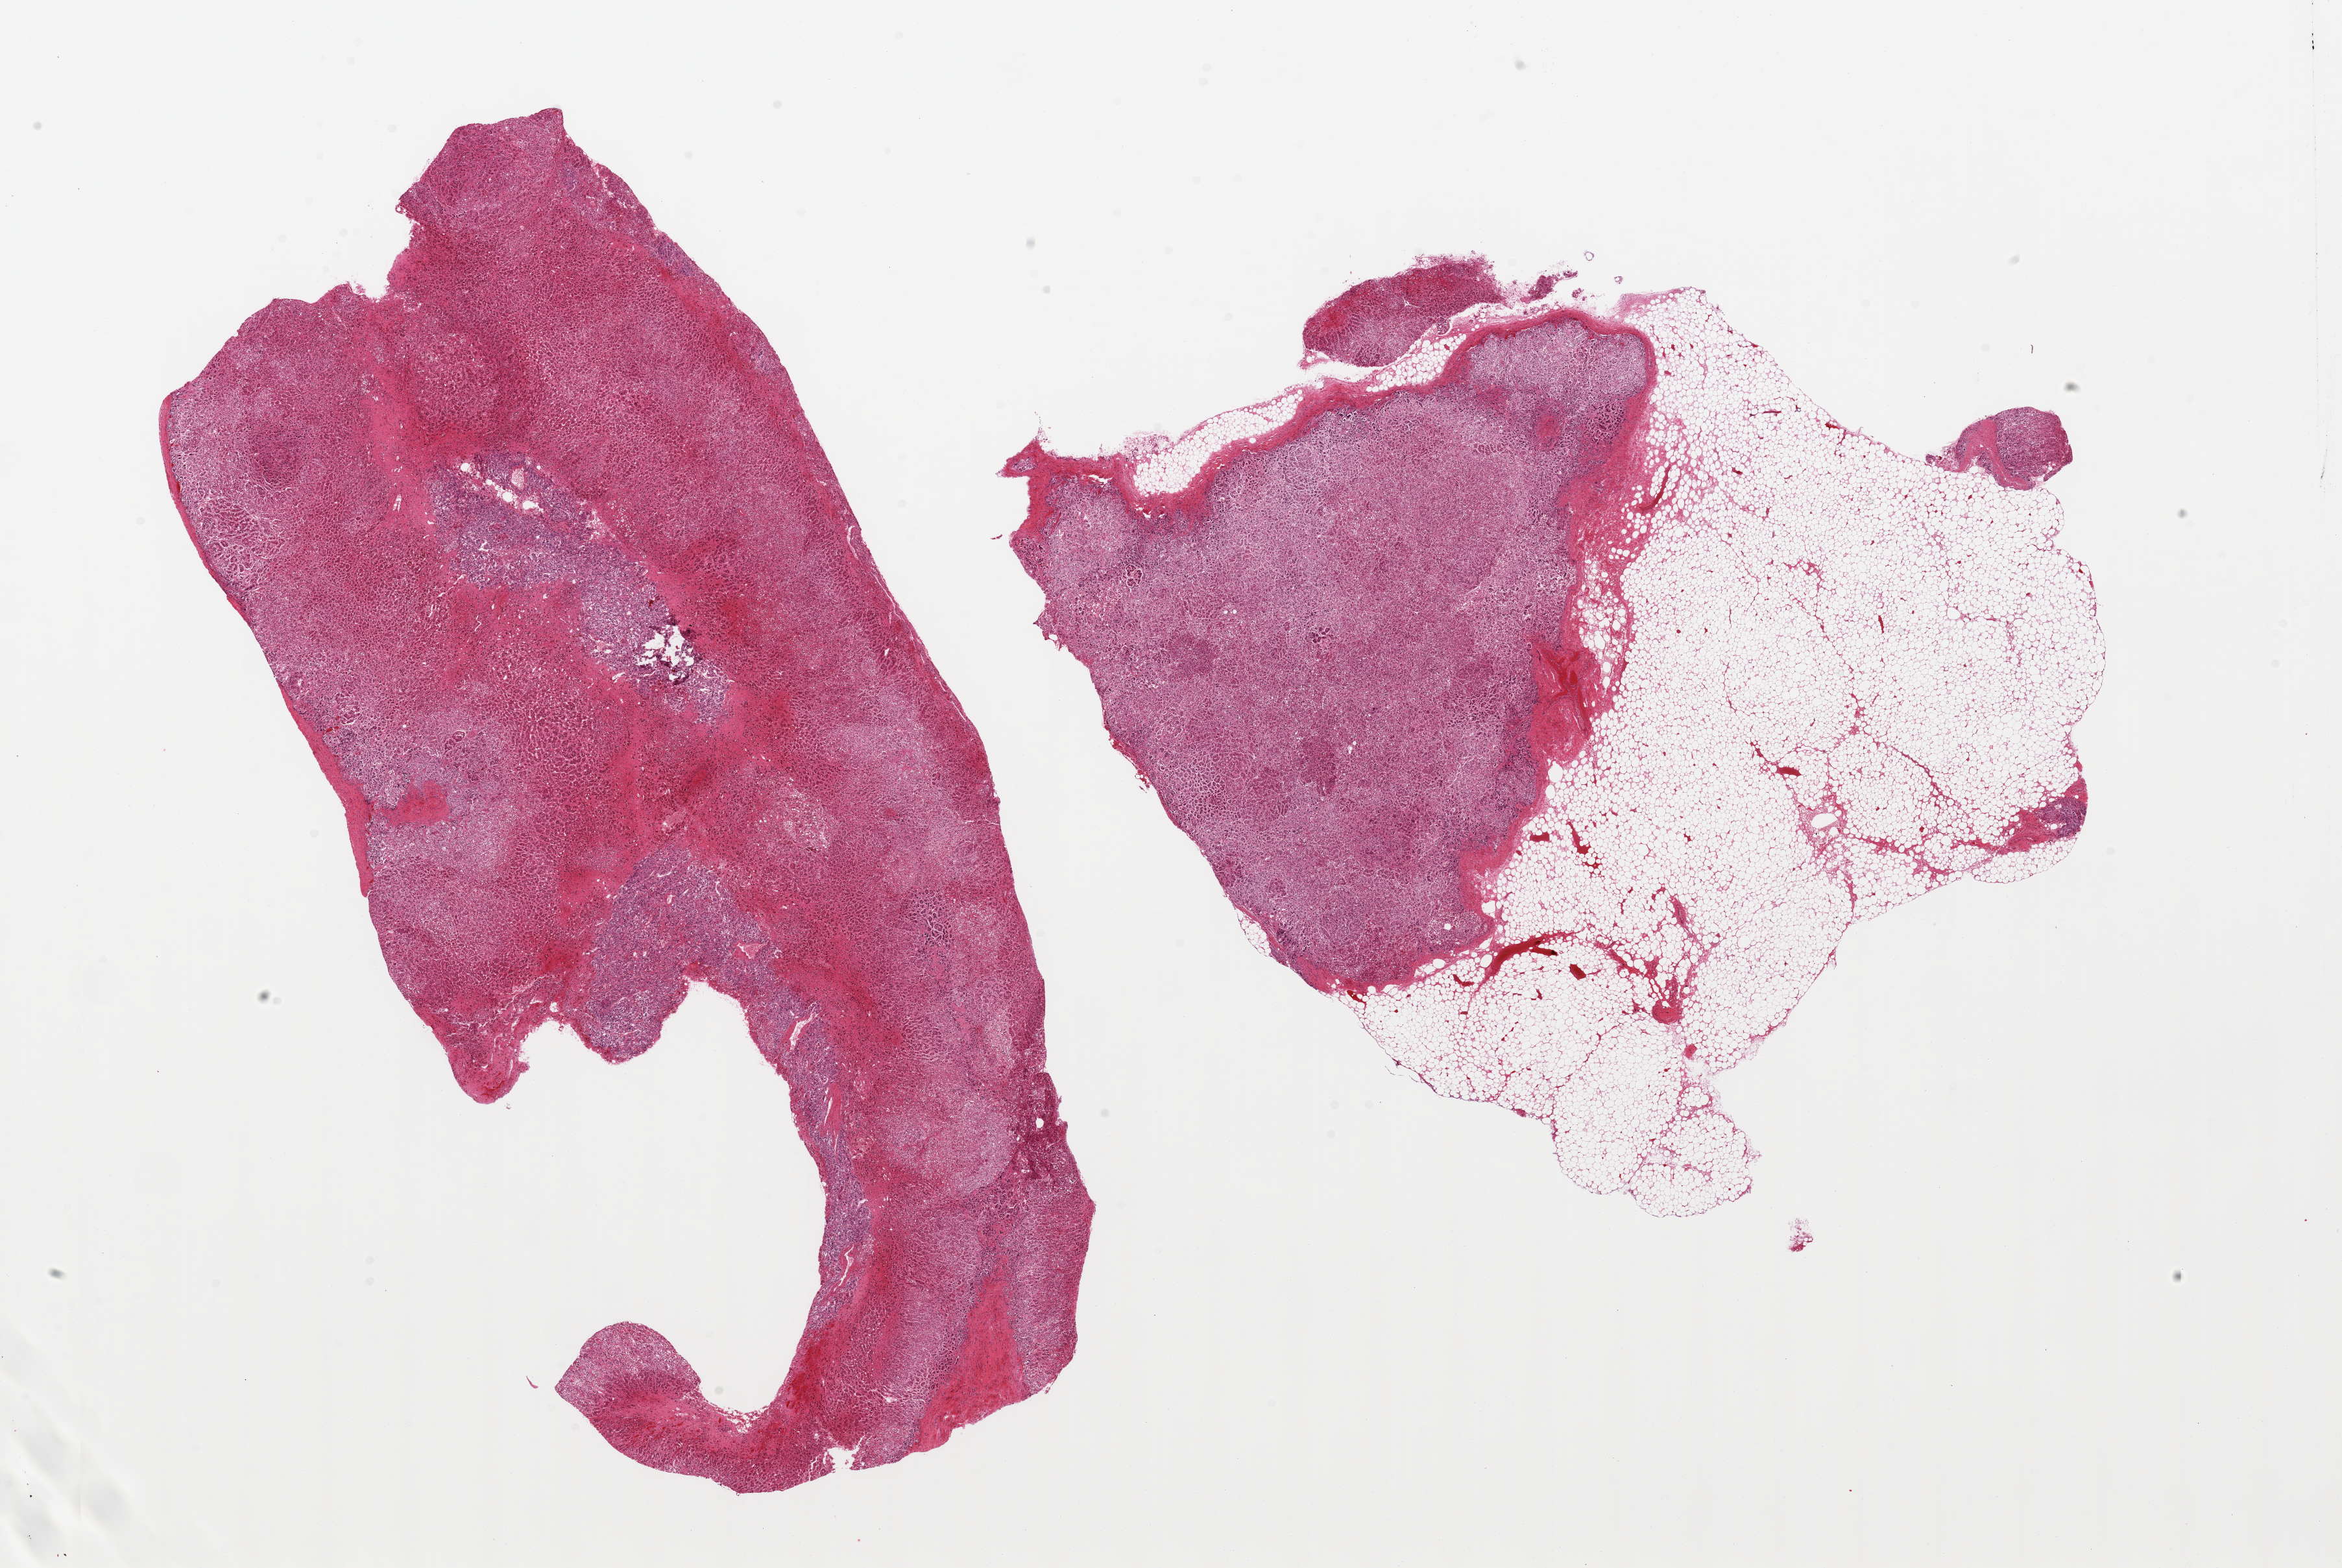
Digitized H&E-stained section, brightfield — low-resolution overview of the scanned area, about 28.5 x 19.1 mm. PAXgene-fixed, paraffin-embedded tissue. Sampled site (target tissue): adrenal gland. Donor tissue sample. Male donor.
Pathologist's review note for this sample: 2 pieces, one piece with 50% external fat.